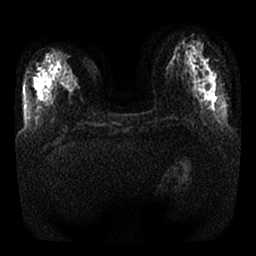
Breast MRI, one axial slice. Position 10 of 32 along the scan axis. Diffusion-weighted series; image 2 of 4 stored at this slice position (different b-values; order by instance number). 1.5 T. 4 mm slice thickness. 256 × 256 image matrix, field of view 350 × 350 mm. Female patient.
Outlined on this slice (outlined manually by an expert reader):
- tumour on diffusion-weighted imaging: box from (x=68, y=77) to (x=75, y=89) px